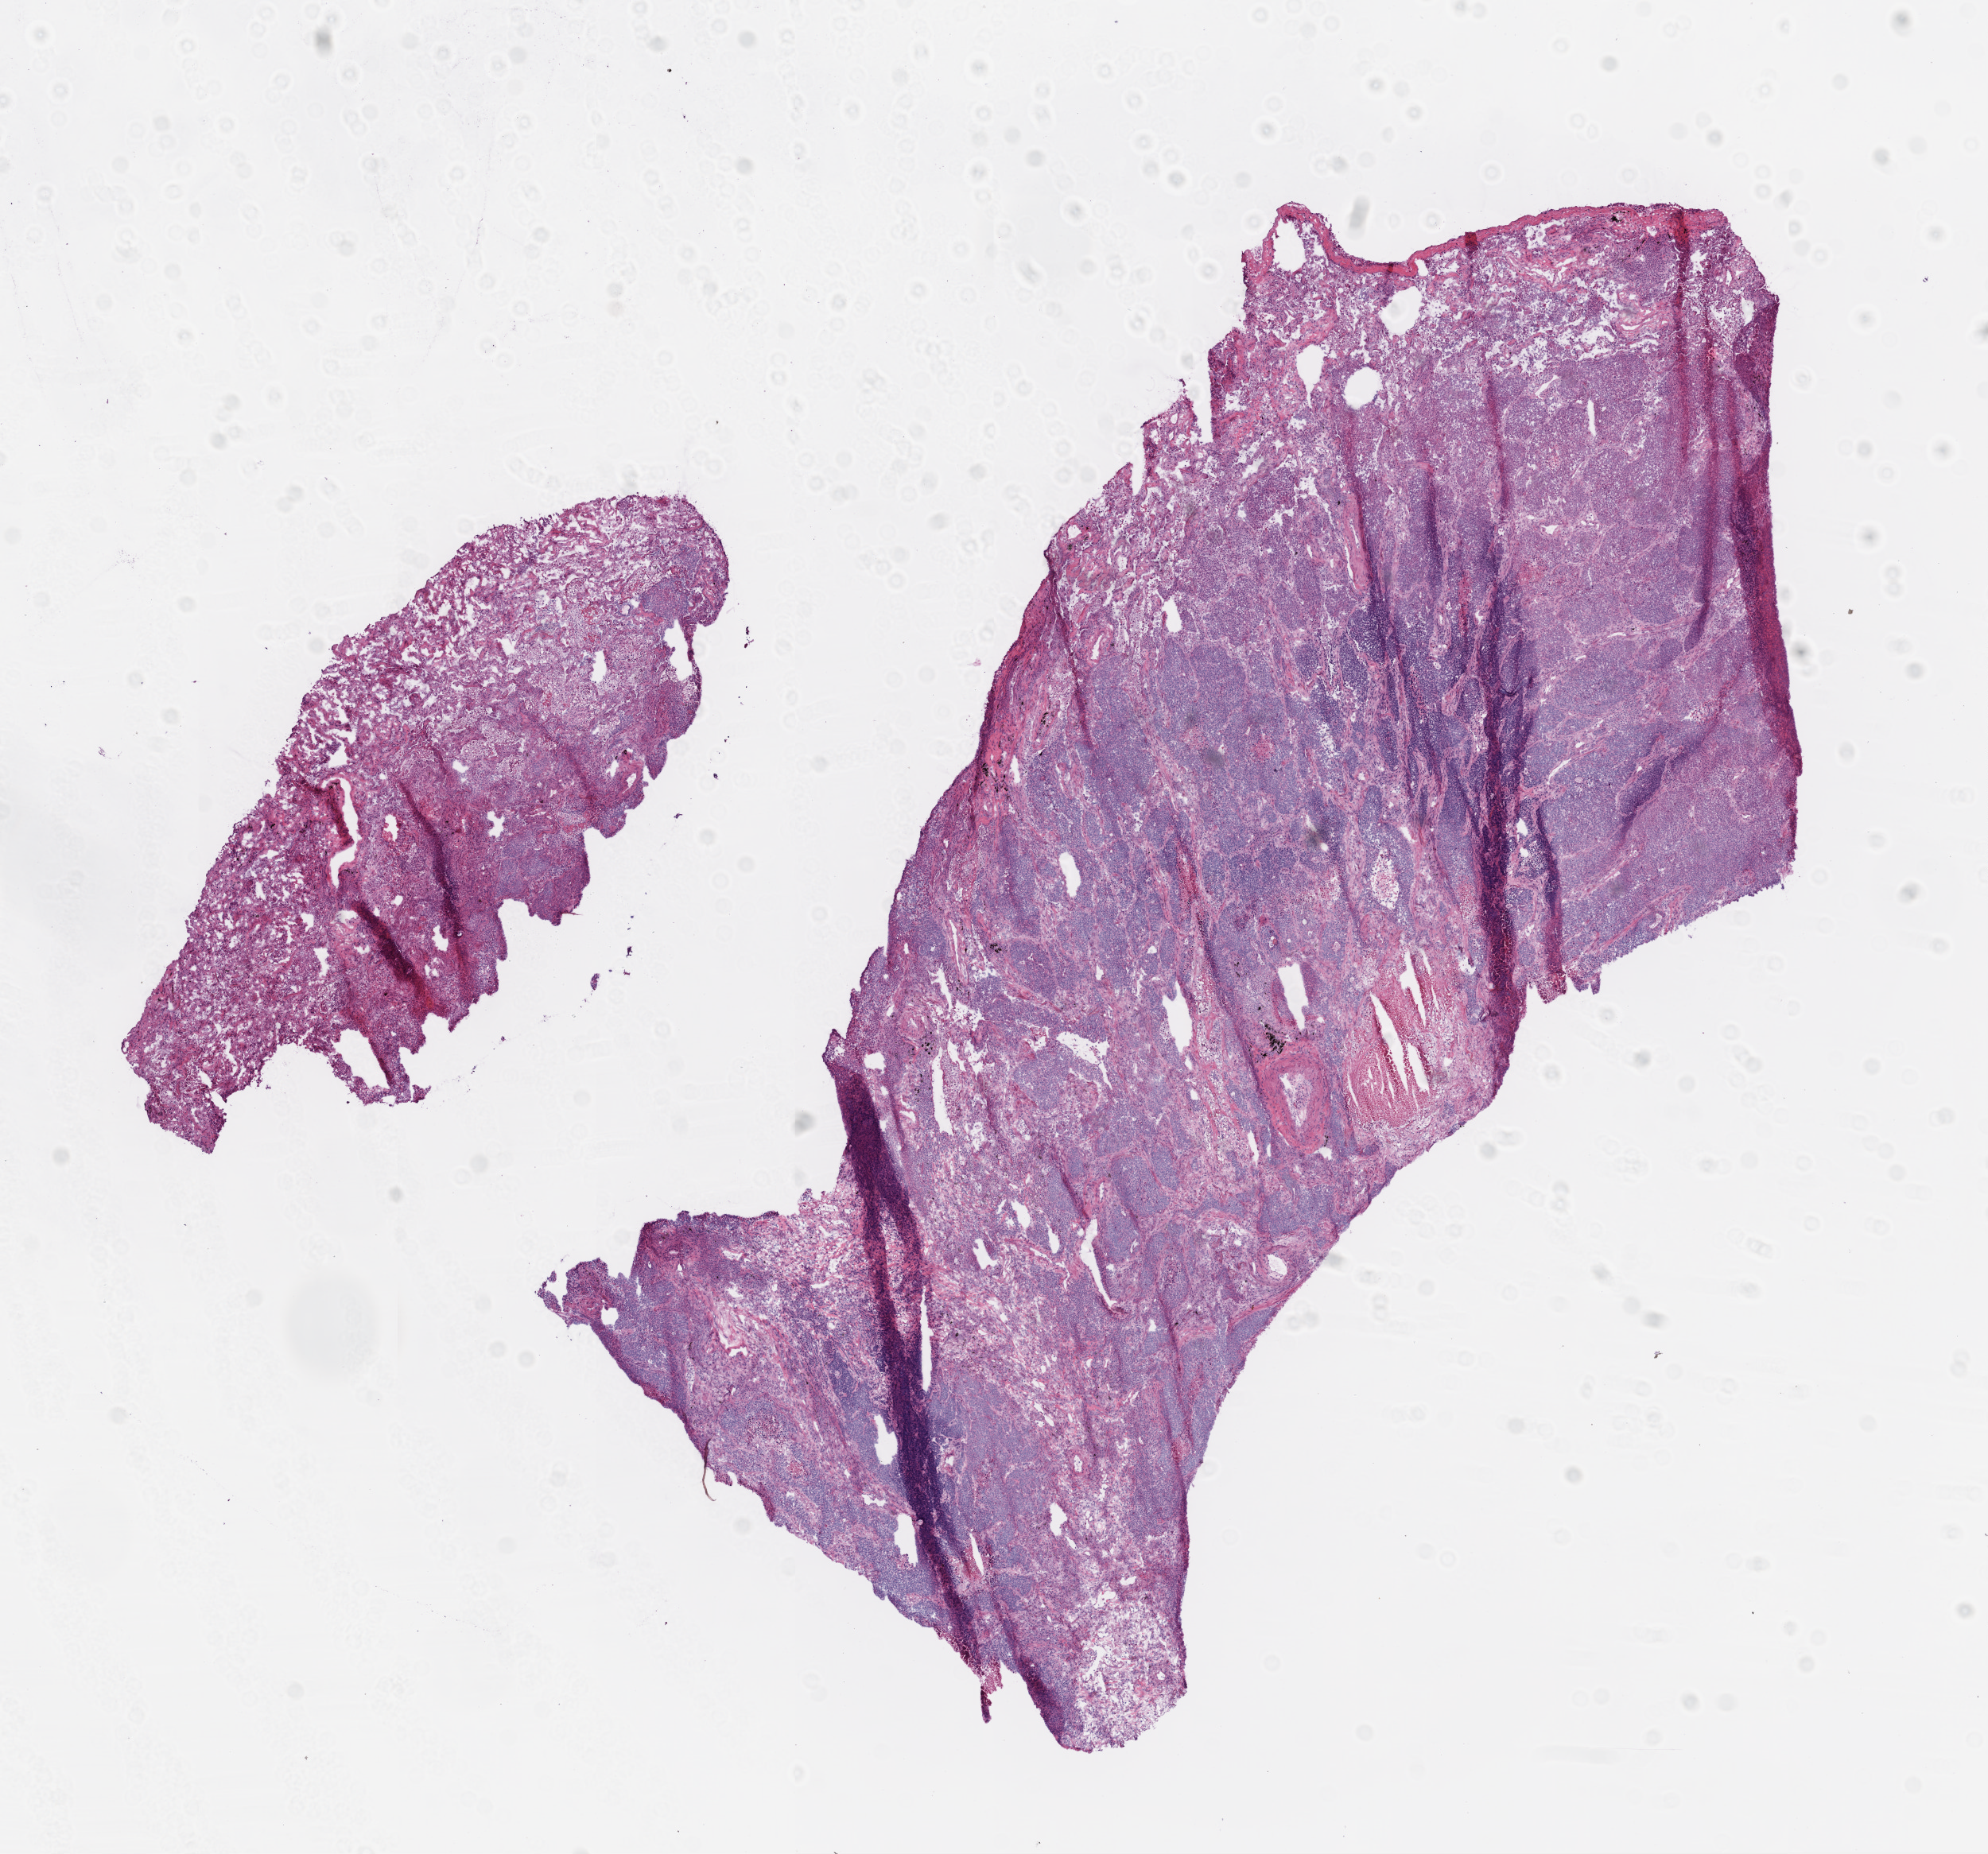
Hematoxylin and eosin (H&E) stained whole-slide image — whole scanned area (about 10.0 x 9.4 mm) shown as a low-resolution overview, frozen section, lung, primary tumour sample. Female patient; age at initial diagnosis 74 years. Composition of this section per pathologist review: tumour cells 80%, tumour nuclei 90%, normal cells 2%, stromal cells 10%, necrosis 8%.
* histologic diagnosis: Basaloid squamous cell carcinoma (upper lobe, lung)
* AJCC pathologic stage: IB